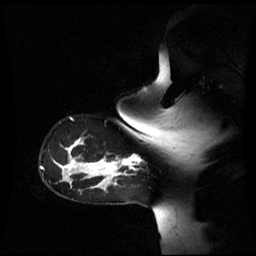
Breast MRI (dynamic contrast-enhanced), one sagittal slice. Dynamic contrast-enhanced series, image 2 of 3 at this slice position (ordered by acquisition). 1.5 T. TE 4.2 ms, TR 8.4 ms. 2.6 mm slice thickness. 256 × 256 image matrix, field of view 270 × 270 mm. Female patient, age 39 years. From the clinical record (not read from this slice): setting: breast cancer imaged before/during neoadjuvant chemotherapy; receptor status: triple-negative.
Annotated regions visible in this slice (semi-automatically segmented with operator editing):
- analysis volume of interest (the breast-tissue region the enhancement analysis was run in; not a lesion): box from (x=105, y=156) to (x=141, y=179) px
- tumour enhancement mask (voxels above the 70 % enhancement threshold inside the analysis volume of interest): (x=105, y=157)–(x=140, y=179)